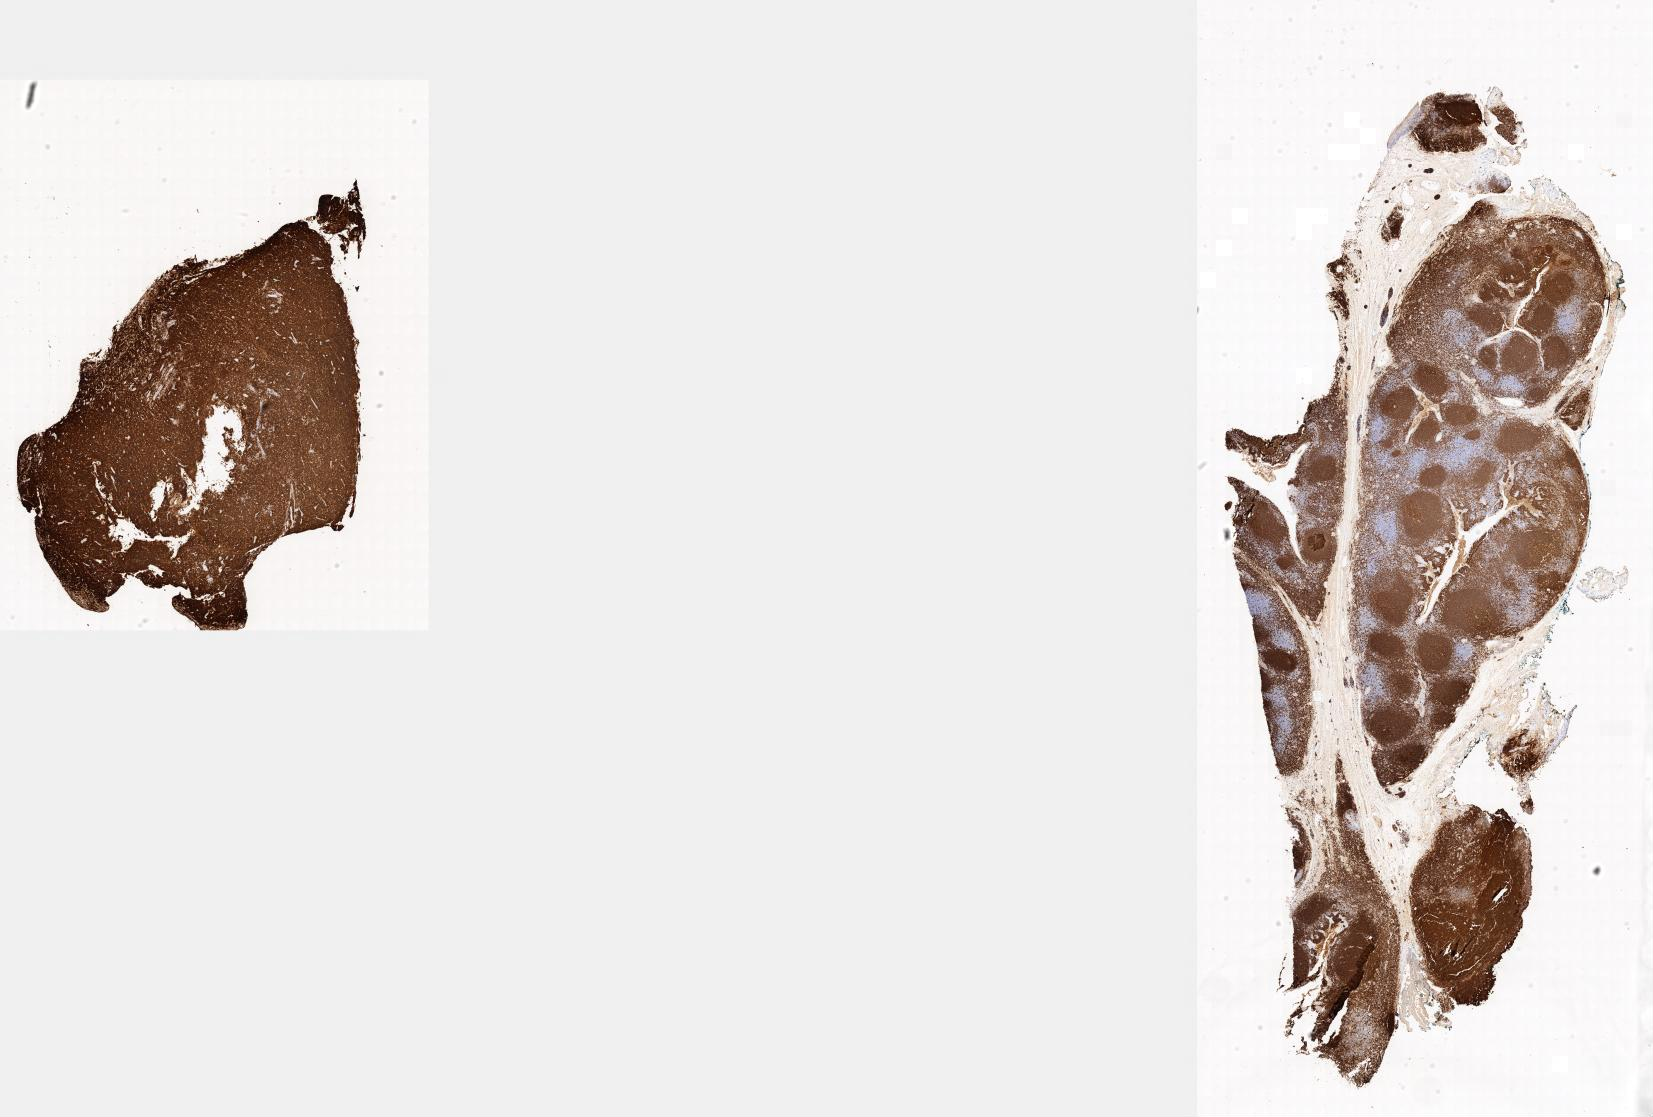
Whole-slide image, immunohistochemical stain for CD20 — whole scanned area shown as a low-resolution overview; specimen: tumor tissue; anatomic site: ovary. Female, age 3 years at initial diagnosis.
Histologic diagnosis: Burkitt lymphoma, NOS.